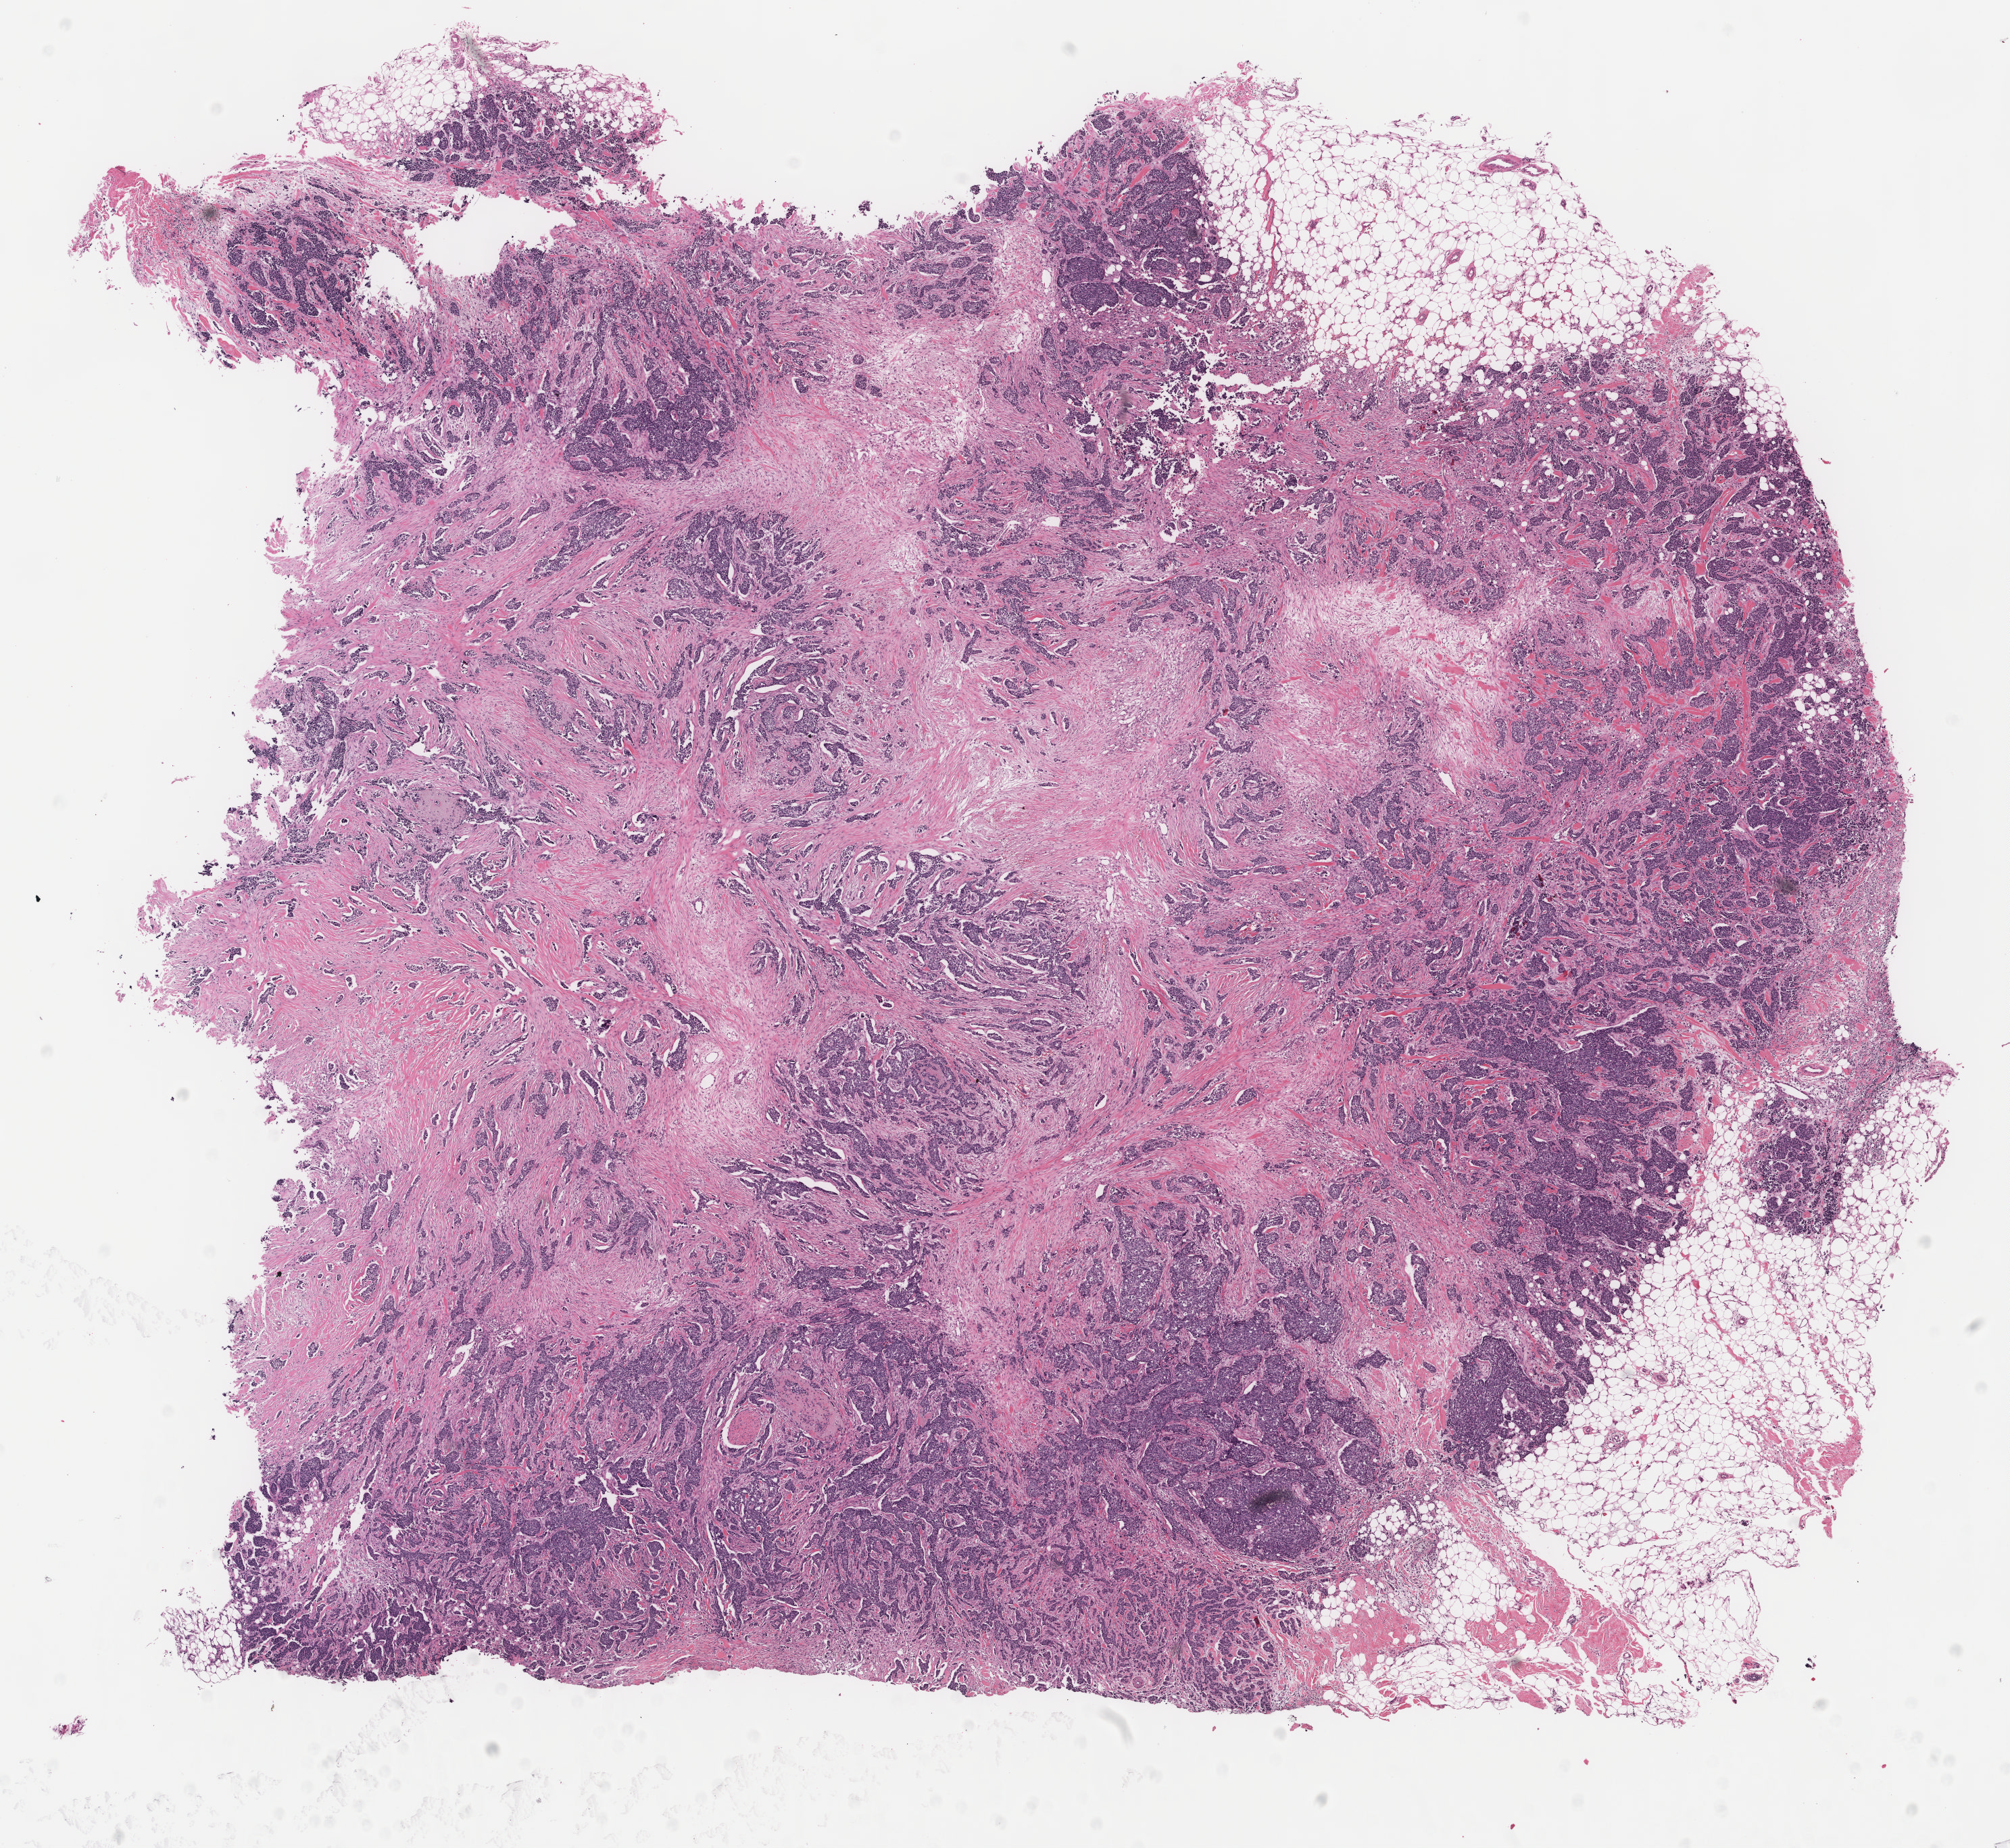
Digitized H&E tissue section (whole slide), whole scanned area (about 11.8 x 10.9 mm) shown as a low-resolution overview; formalin-fixed paraffin-embedded (FFPE) diagnostic section; breast, primary tumour sample. Patient: female, age at initial diagnosis 55 years.
Diagnosis: Infiltrating duct carcinoma, NOS. Lymph nodes positive (case pathology): 0 of 11 examined. AJCC pathologic stage: IA (7th edition).